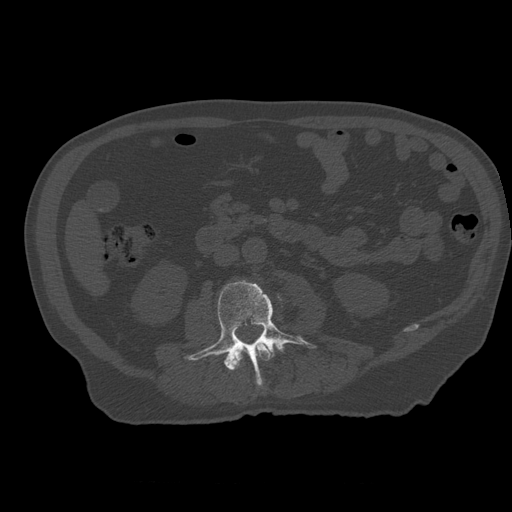
CT including the spine, one axial slice; slice 192 of 399 in the series (ordered by position); reconstruction kernel STANDARD; 120 kVp; bone window (W 1800 / L 400 HU); 1.25 mm slice thickness; 512 × 512 image matrix. Patient age 73 years. Case-level facts recorded for this patient, not image findings: primary cancer: prostate; vertebrae with lytic lesions (as recorded): L2.
Outlined on this slice (semi-automatic segmentation, software-assisted and operator-edited):
- L2 vertebra: bounding box [x1, y1, x2, y2] px = [232, 343, 272, 369]
- L3 vertebra: [185, 281, 315, 387]